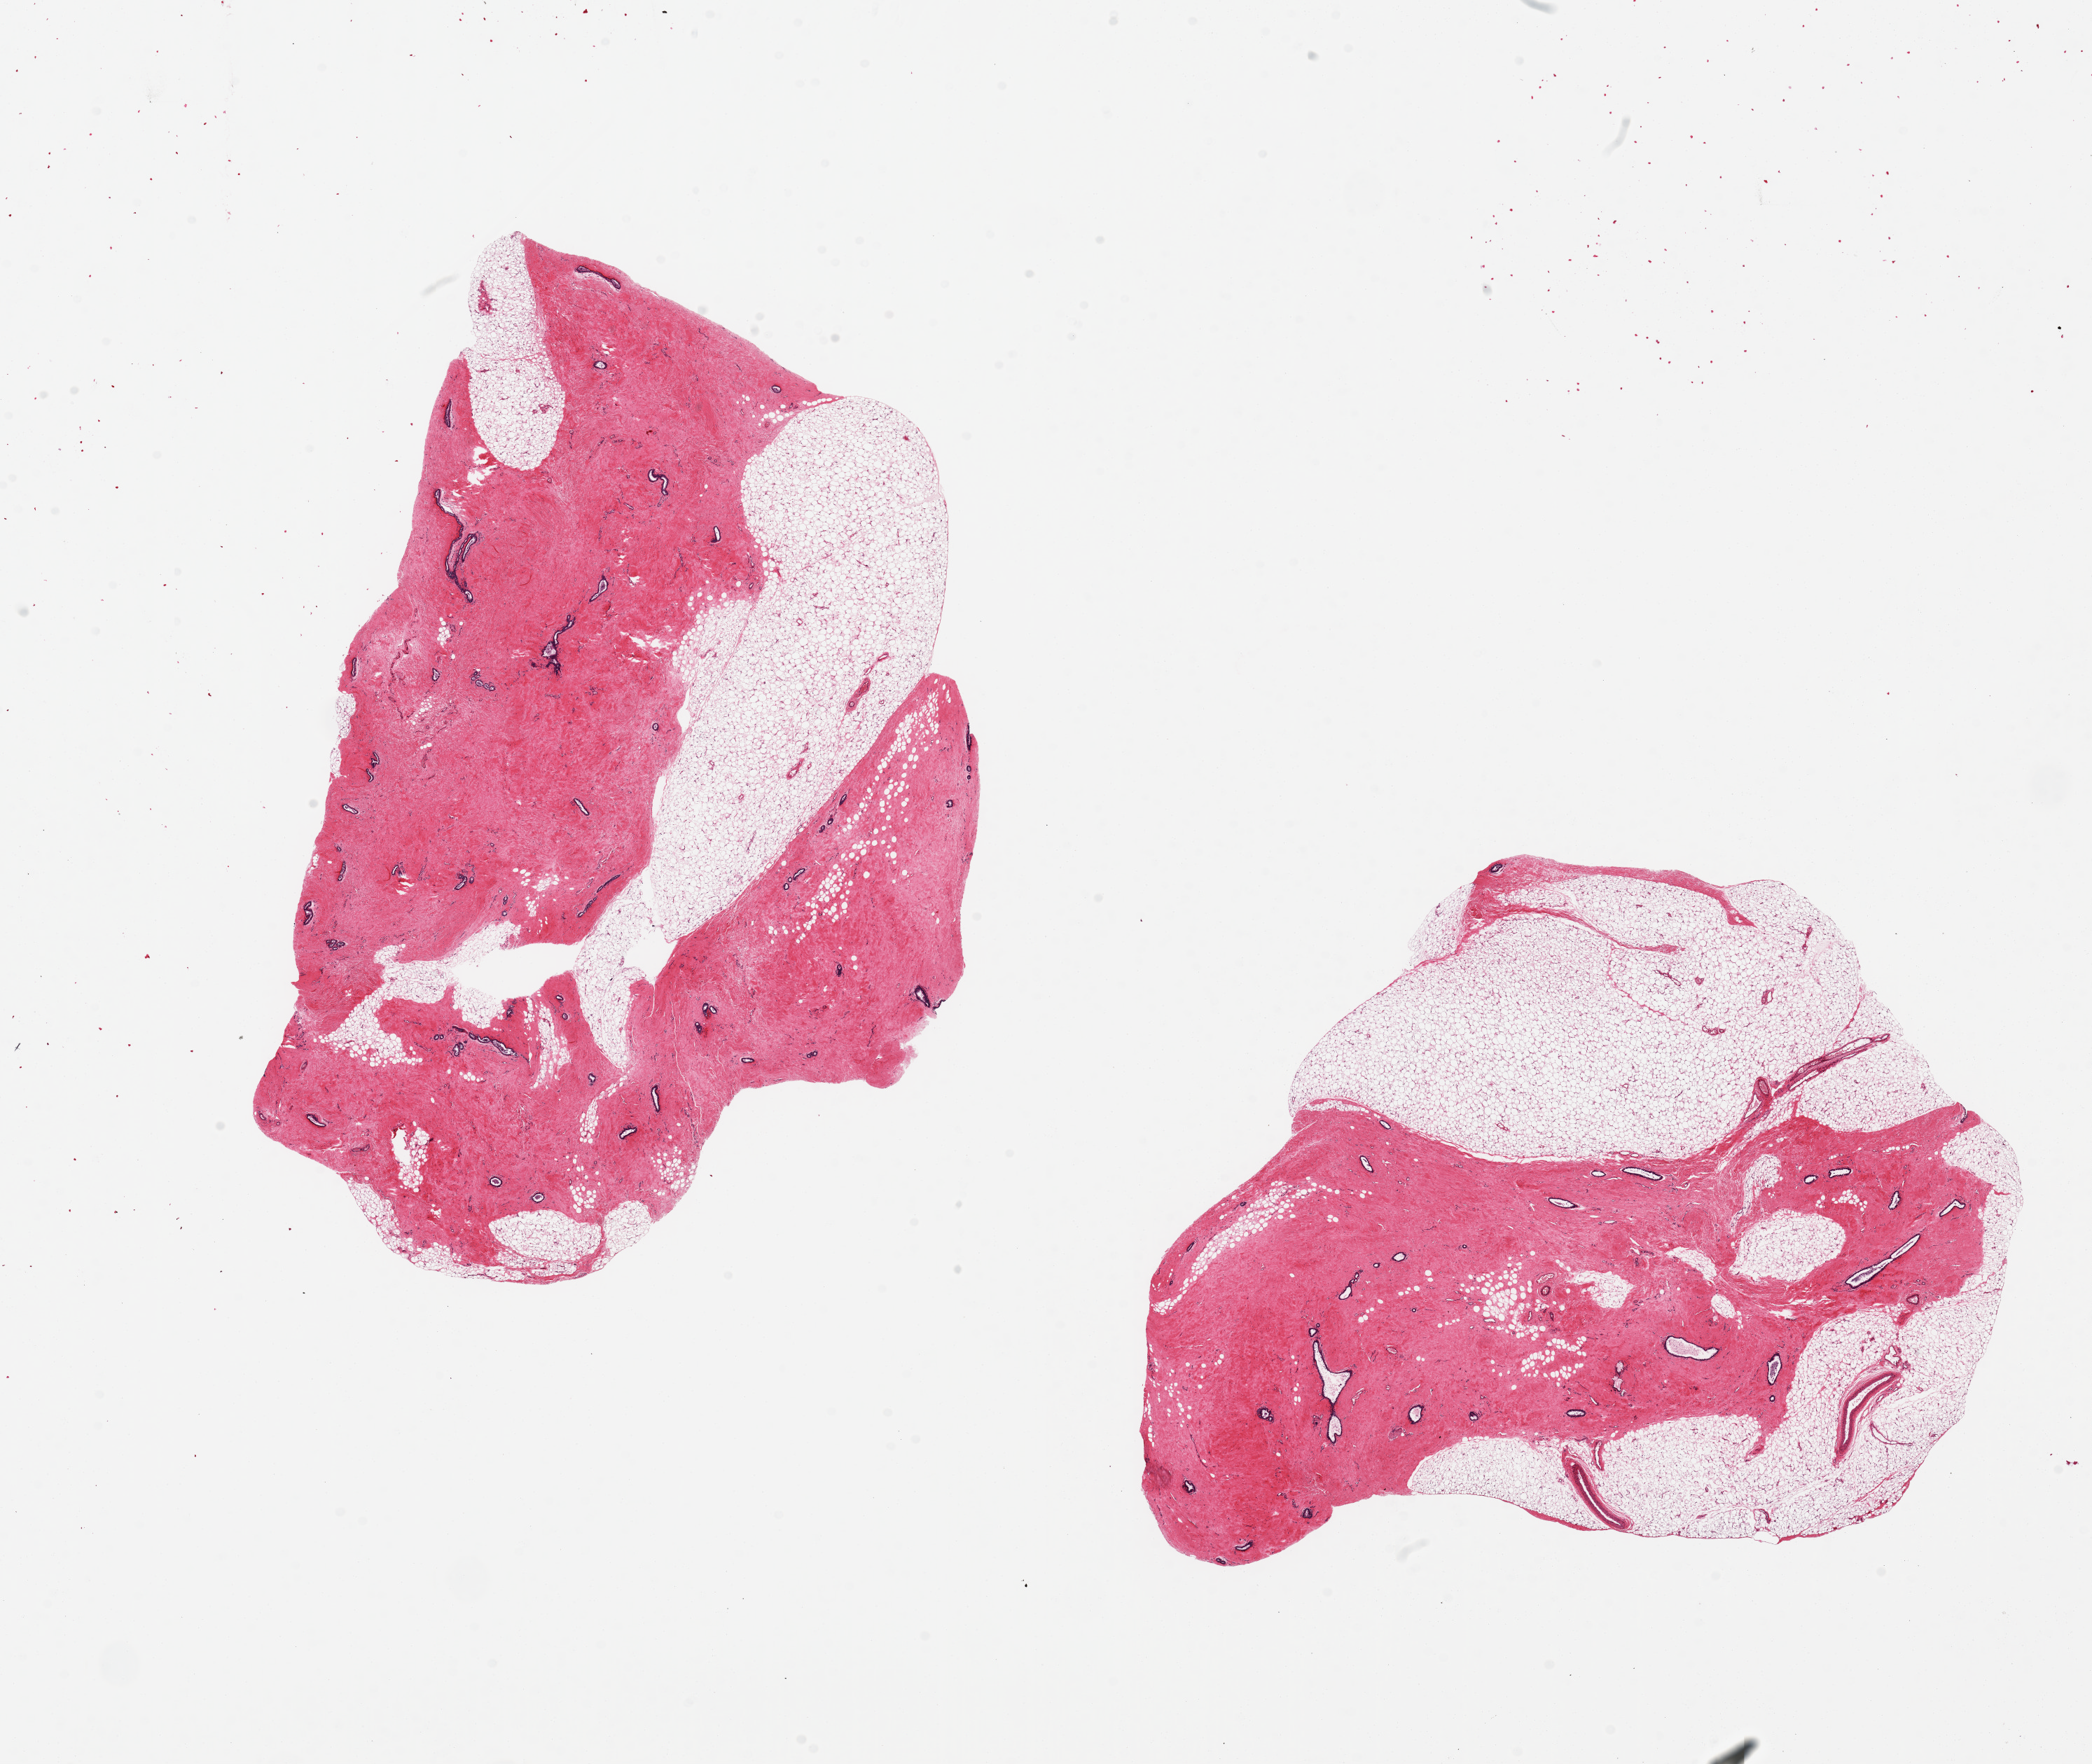
Whole-slide image, H&E stain, whole scanned area (about 23.6 x 19.9 mm, from a 20x scan) shown as a low-resolution overview, PAXgene-fixed, paraffin-embedded tissue, sampled site (target tissue): breast, tissue donor sample. Donor sex: male.
• reviewer comment on this tissue sample: 2 pieces 10x8 & 10x7 mm; gynecomastia with ~50-60% fibrous tissue containing ducts and the remainder adipose